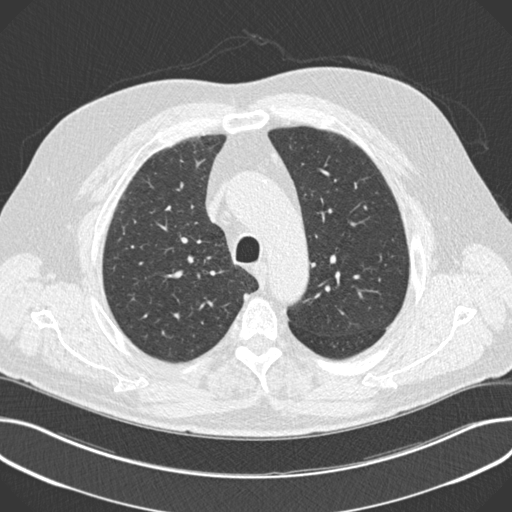
Axial slice from a low-dose chest CT screening exam. First (baseline) screen. Lung window (W 1500 / L -600 HU). 2 mm slice thickness. Slice 47 of 202 in the series. Male, age 64 years at enrolment. Current smoker at enrolment.
- Expert reader's lesion annotation, bounding box <111,200,139,227> (left, top, right, bottom; pixels).
- Screening reader's record for this exam: no non-calcified nodule ≥4 mm recorded.
- Official screen result: negative screen, no significant abnormalities.